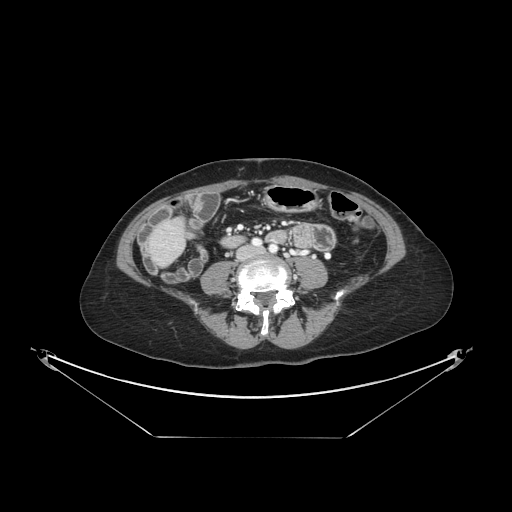
Contrast-enhanced abdominal CT, one axial slice; position 22 of 148 along the scan axis; 120 kVp; intravenous contrast given; soft-tissue window (W 400 / L 40 HU); 2.5 mm slice thickness; 512 × 512 image matrix. Female patient, age 73 years. From the clinical record (not read from this slice): diagnosis: colorectal cancer liver metastases, imaged before liver resection; multiple liver metastases: no; largest metastasis: 1 cm; chemotherapy before resection: yes.
Annotated regions visible in this slice (expert manual segmentation):
- liver: bounding box [x1, y1, x2, y2] px = [153, 221, 184, 264]
- planned liver remnant (the part of the liver to remain after resection): [171, 221, 180, 228]